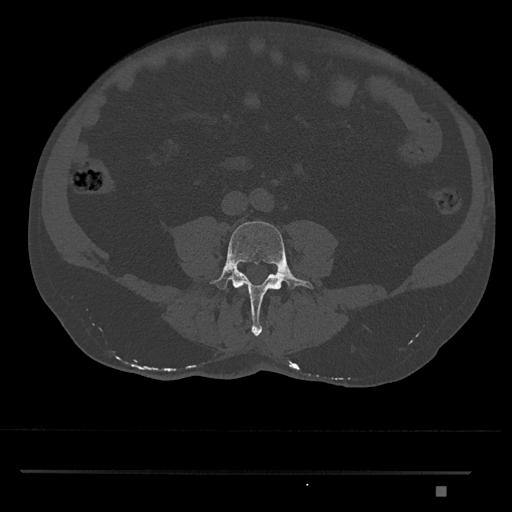
CT including the spine, one axial slice. Position 618 of 1134 along the scan axis. 120 kVp. Bone window (W 1800 / L 400 HU). 0.5 mm slice thickness. 512 × 512 image matrix, field of view 429 × 429 mm. Male patient, age 65 years. Case-level facts recorded for this patient, not image findings: primary cancer: prostate.
Annotated regions visible in this slice (semi-automatically segmented with operator editing):
- L4 vertebra: bounding box (x1, y1, x2, y2) in pixels: (210, 221, 314, 336)